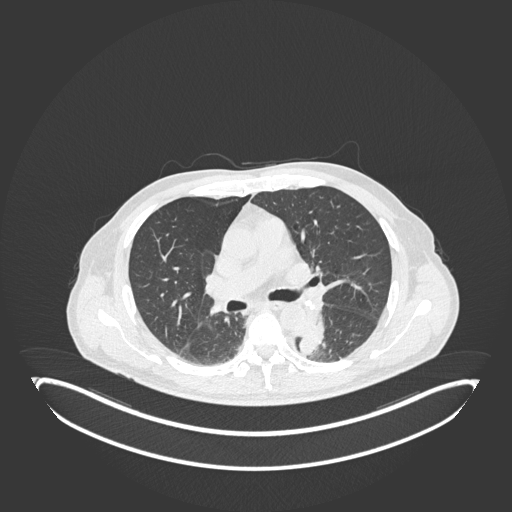
Chest CT, one axial slice; position 124 of 251 along the scan axis; reconstruction kernel B30f; lung window (W 1500 / L -600 HU); 1 mm slice thickness; 512 × 512 image matrix, field of view 500 × 500 mm. Patient: male, 72 years. From the clinical record (not read from this slice): clinical TNM (as recorded): T2b N0 M1.
Outlined on this slice (bounding box drawn by a radiologist):
- lung tumour (recorded histology: adenocarcinoma): bounding box (x1, y1, x2, y2) in pixels: (298, 314, 331, 355)